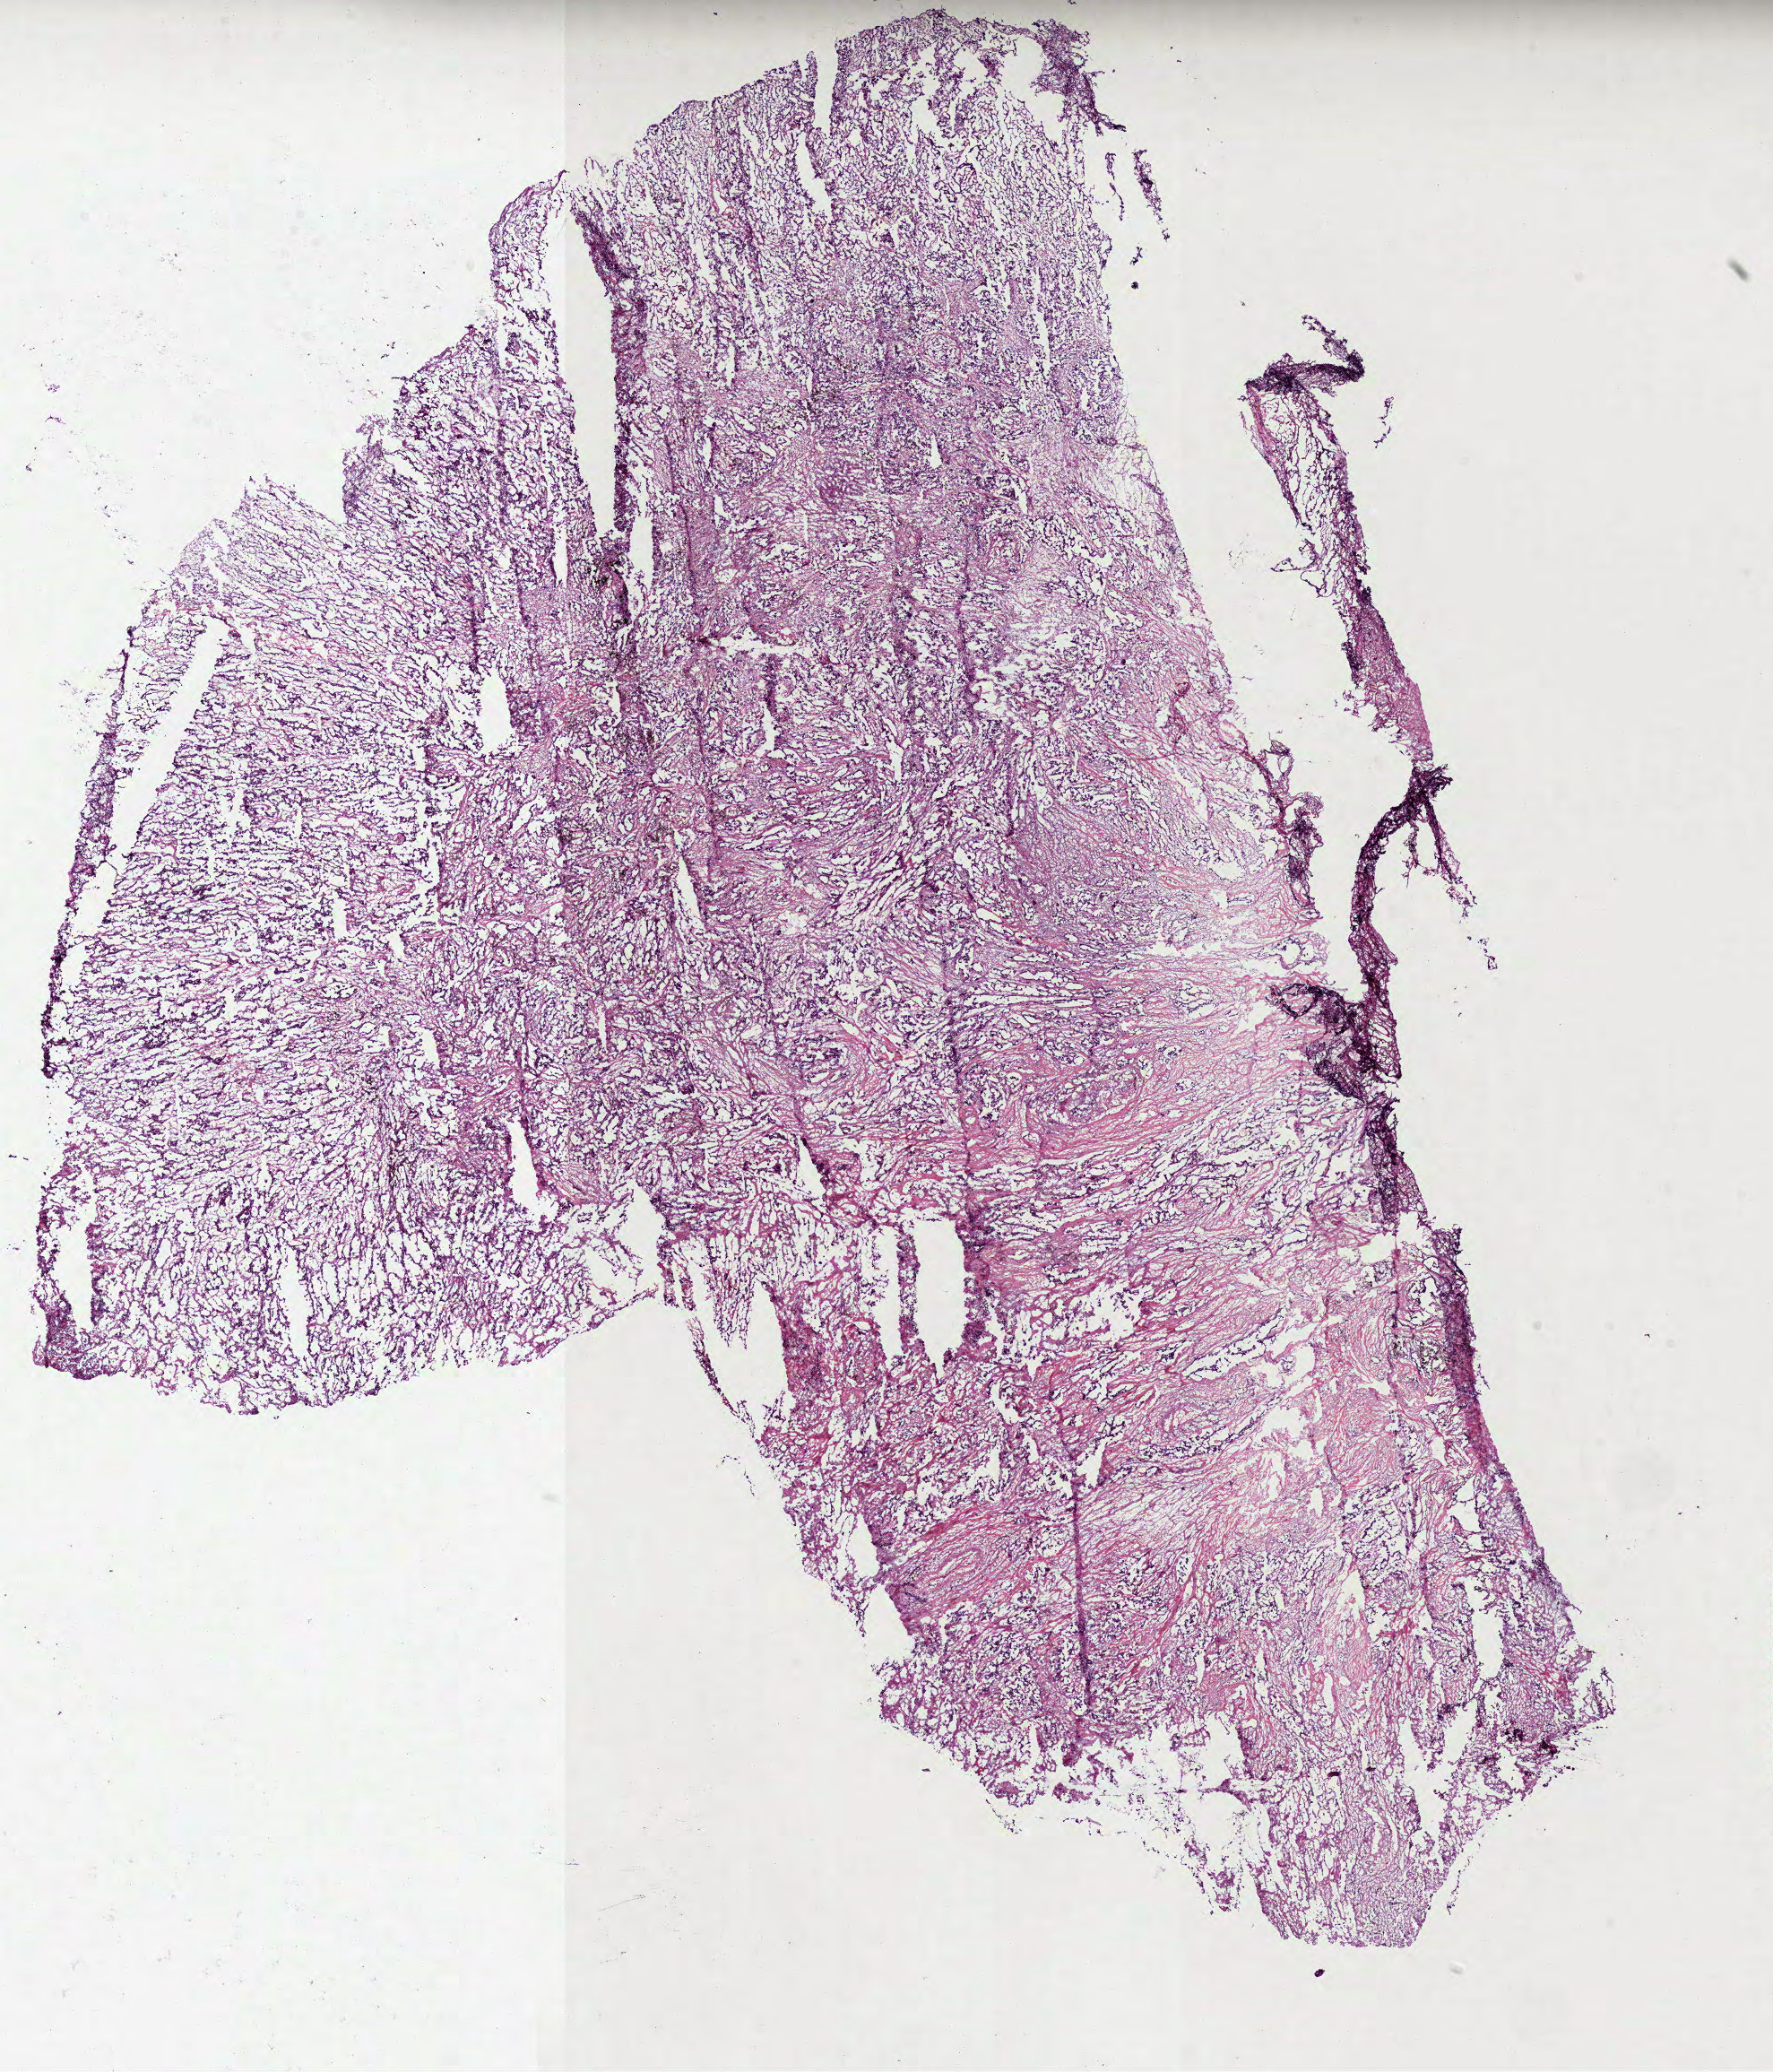
Whole-slide histology image, Hematoxylin and eosin (H&E) stained — whole scanned area (about 16.0 x 18.6 mm, from a 40x scan) shown as a low-resolution overview; frozen section from the top of the tissue portion; primary tumour sample from the lung. Male patient; age at initial diagnosis 46 years. Pathologist review of this section (percent, as recorded): tumour cells 85%, tumour nuclei 80%, normal cells 0%, stromal cells 15%, necrosis 0%.
Pathologic diagnosis: Adenocarcinoma, NOS (upper lobe, lung). Laterality: right. AJCC pathologic stage: IIA.